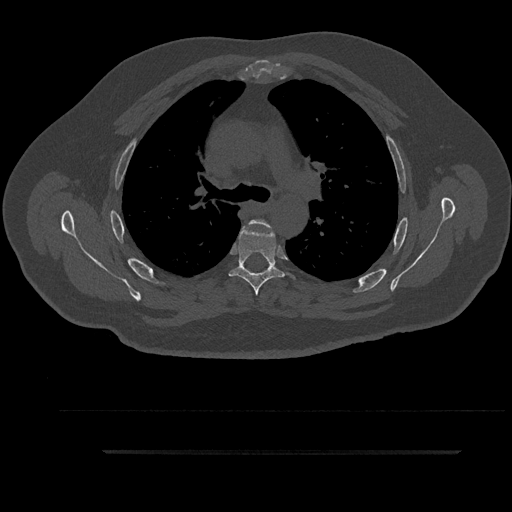
CT including the spine, one axial slice. Slice 631 of 797 in the series (ordered by position). Reconstruction kernel Br40s/3. Bone window (W 1800 / L 400 HU). 0.5 mm slice thickness. 512 × 512 image matrix, field of view 432 × 432 mm. Patient: male, 63 years. From the clinical record (not read from this slice): primary cancer: renal.
Outlined on this slice (semi-automatic segmentation, software-assisted and operator-edited):
- T4 vertebra: bounding box <248,219,272,229> (left, top, right, bottom; pixels)
- T5 vertebra: <229,223,296,296>
- T6 vertebra: <261,268,269,274>